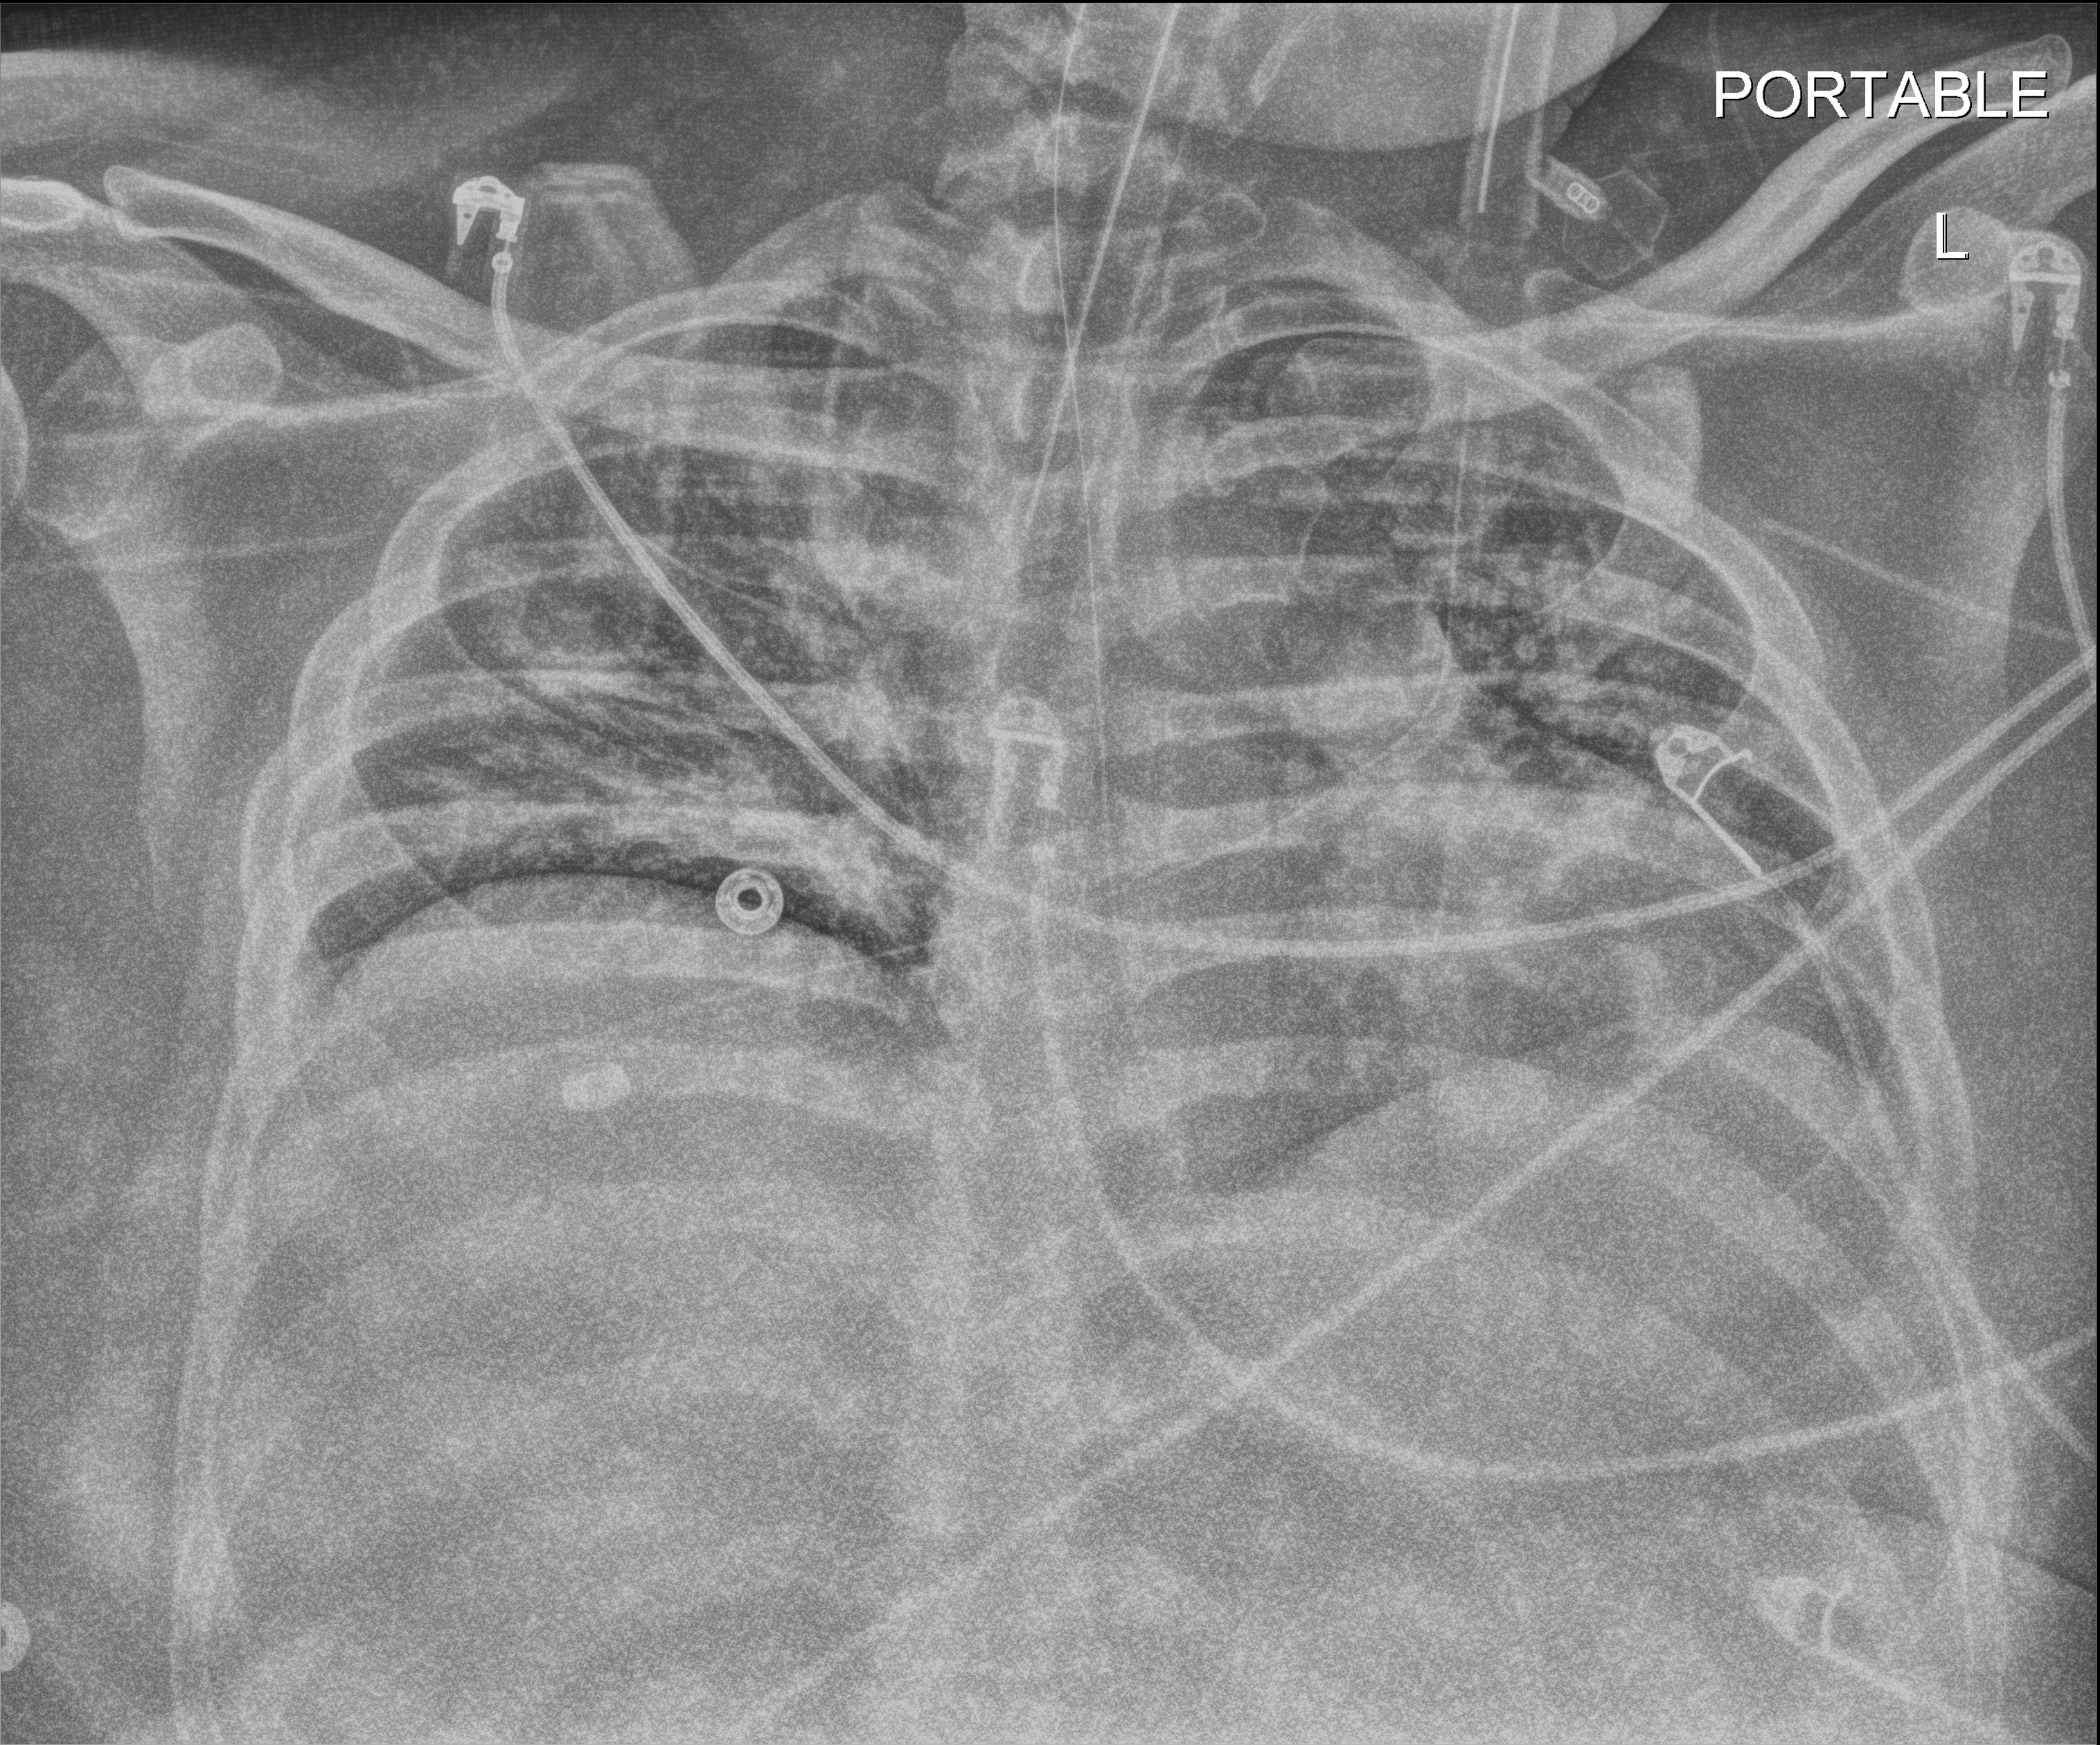
Portable chest radiograph, anteroposterior (AP) projection. Male patient hospitalised with COVID-19, age 18–59 years.
Admission-level facts for this patient (not findings on this image; timing relative to this image not recorded): chronic kidney disease (admission record): no.